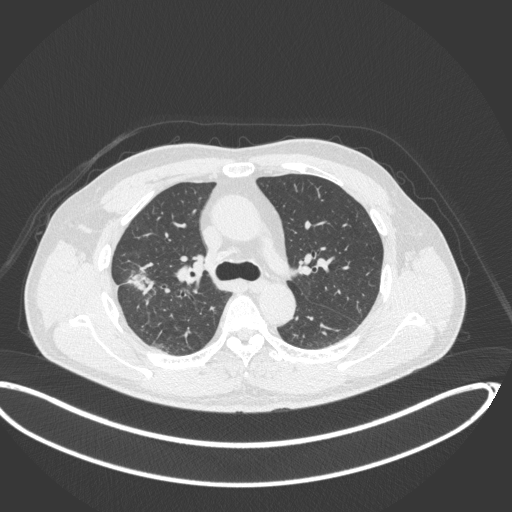
Chest CT, one axial slice. Slice 226 of 341 in the series (ordered by position). Reconstruction kernel B31f. 120 kVp. Lung window (W 1500 / L -600 HU). 512 × 512 image matrix, field of view 439 × 439 mm. Male patient, age 63 years. From the clinical record (not read from this slice): clinical TNM (as recorded): T1c N0 M0; histopathological grade: G2-3.
Annotated regions visible in this slice (bounding box drawn by a radiologist):
- lung tumour (recorded histology: adenocarcinoma): bounding box (x1, y1, x2, y2) in pixels: (118, 255, 158, 302)